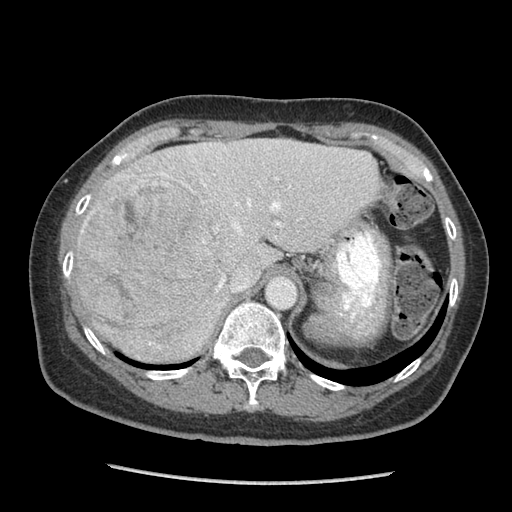
Contrast-enhanced abdominal CT (liver protocol), one axial slice. Position 63 of 105 along the scan axis. Reconstruction kernel STANDARD. Soft-tissue window (W 400 / L 40 HU). 2.5 mm slice thickness. 512 × 512 image matrix, field of view 340 × 340 mm. Case-level facts recorded for this patient, not image findings: diagnosis: hepatocellular carcinoma (patient treated with transarterial chemoembolisation; whether this scan precedes or follows treatment is not stated here); TNM stage (as recorded): Stage-I; Child-Pugh class: A; tumour nodularity: uninodular; tumour size: 11.1 cm.
Structures marked on this image (semi-automatically segmented with operator editing):
- abdominal aorta: bounding box <268,277,296,307> (left, top, right, bottom; pixels)
- liver parenchyma outside the tumour (the mass and vessels are separate outlines, so this box may not span the whole liver): <76,138,380,362>
- mass: <77,170,223,346>
- liver vessels: <82,144,291,288>